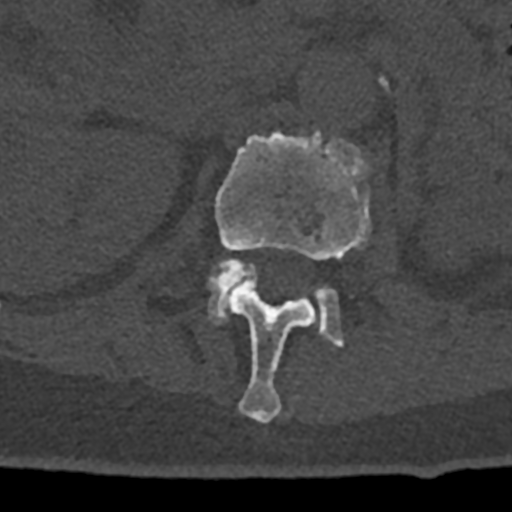
CT including the spine, one axial slice; position 419 of 797 along the scan axis; reconstruction kernel Br40s/3; bone window (W 1800 / L 400 HU); 0.5 mm slice thickness; 512 × 512 image matrix, field of view 160 × 160 mm. Male patient, age 74 years. From the clinical record (not read from this slice): primary cancer: renal; vertebrae with lytic lesions (as recorded): T10, L1, L2, L3, L4, L5.
Structures marked on this image (semi-automatic segmentation, software-assisted and operator-edited):
- L1 vertebra: bounding box [x1, y1, x2, y2] px = [215, 131, 371, 423]
- L2 vertebra: [208, 259, 344, 347]